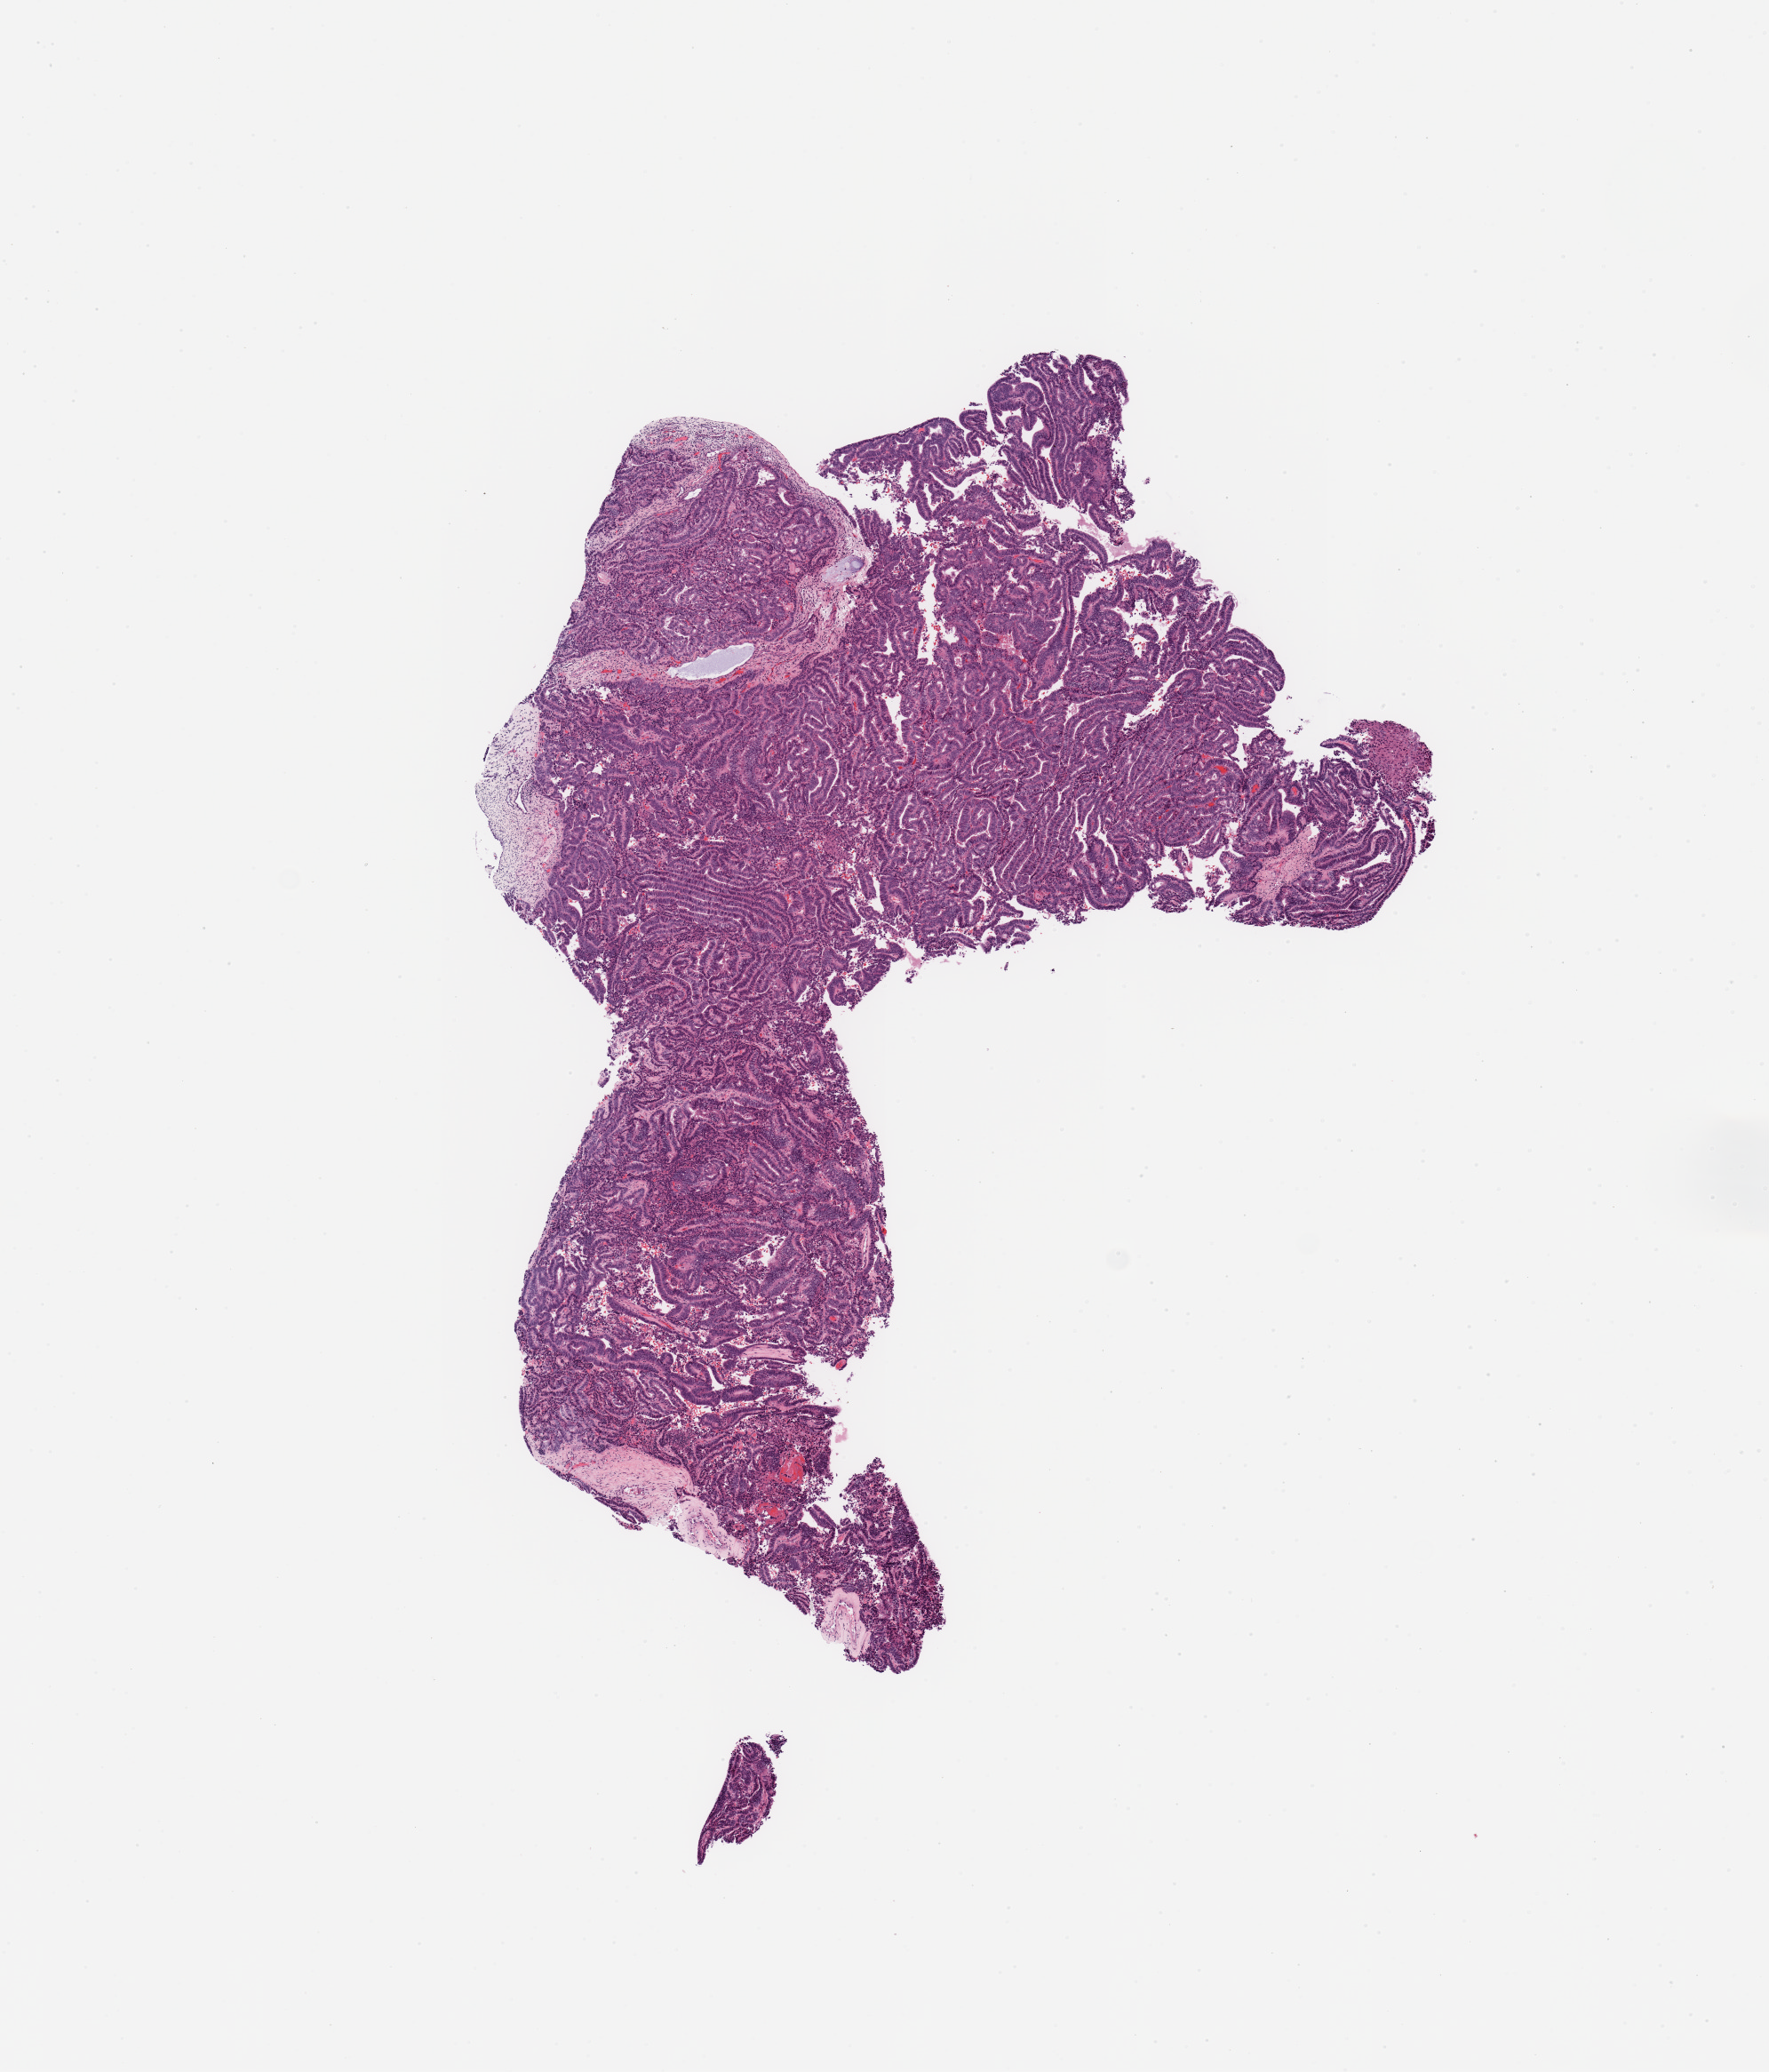
Digitized H&E tissue section (whole slide) — whole scanned area (about 7.9 x 9.2 mm) shown as a low-resolution overview, tumour tissue sample, sampled site: uterus. 62-year-old female patient. Histologic grade: G1 (well differentiated). Pathologist review of this section (percent, as recorded): tumour nuclei 95%, necrosis 0%.
Diagnosis: Endometrioid adenocarcinoma, NOS. AJCC pathologic stage: I.